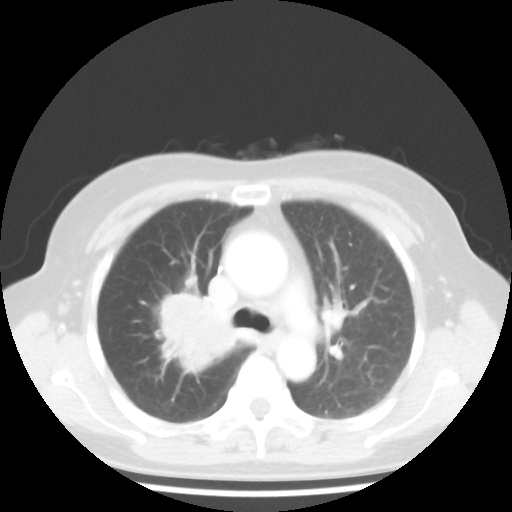
Chest CT, one axial slice; slice 29 of 44 in the series (ordered by position); reconstruction kernel STANDARD; lung window (W 1500 / L -600 HU); 512 × 512 image matrix, field of view 316 × 316 mm. Female patient, age 62 years. Case-level facts recorded for this patient, not image findings: clinical TNM (as recorded): T3 N0 M0; histopathological grade: G3.
Outlined on this slice (rectangle marked by the reading radiologist):
- lung tumour (recorded histology: small cell carcinoma): bounding box (x1, y1, x2, y2) in pixels: (151, 286, 243, 370)